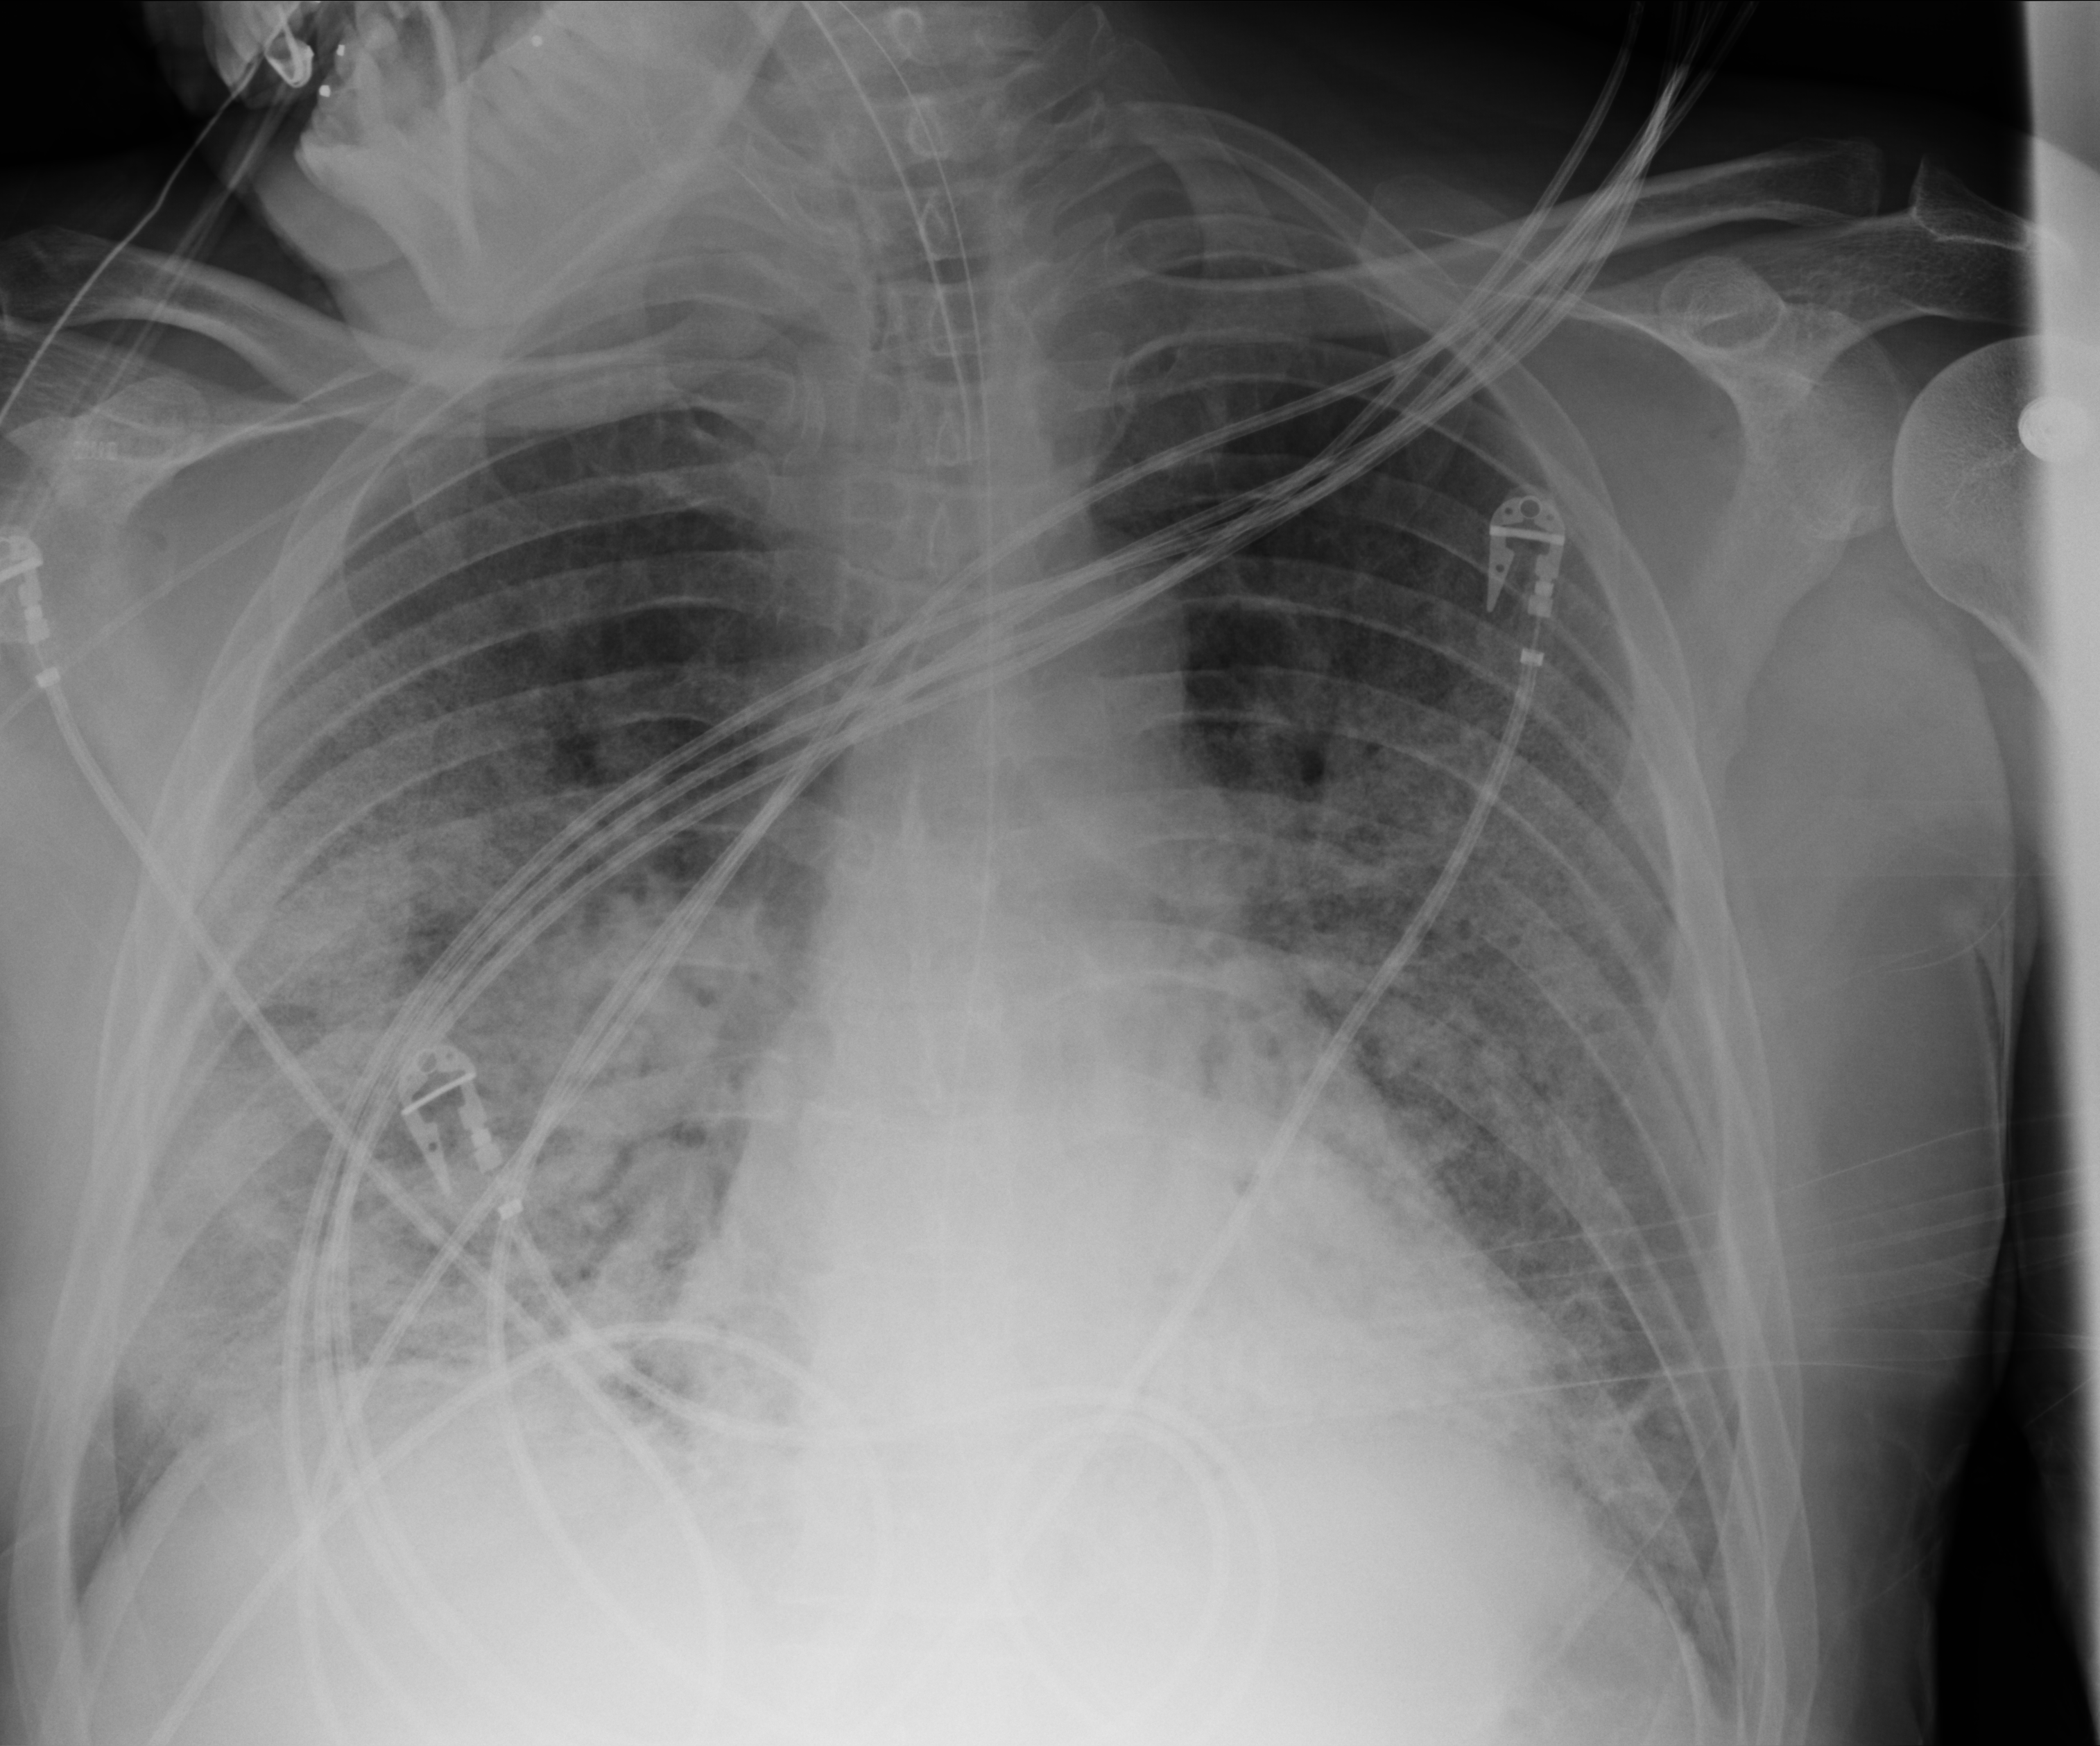
Chest X-ray (portable), anteroposterior (AP) projection. Patient hospitalised with COVID-19; male, aged 18–59 years.
From the hospital-stay record, not from the radiograph (when in the stay this image was taken is not recorded):
- length of hospital stay: 75 days